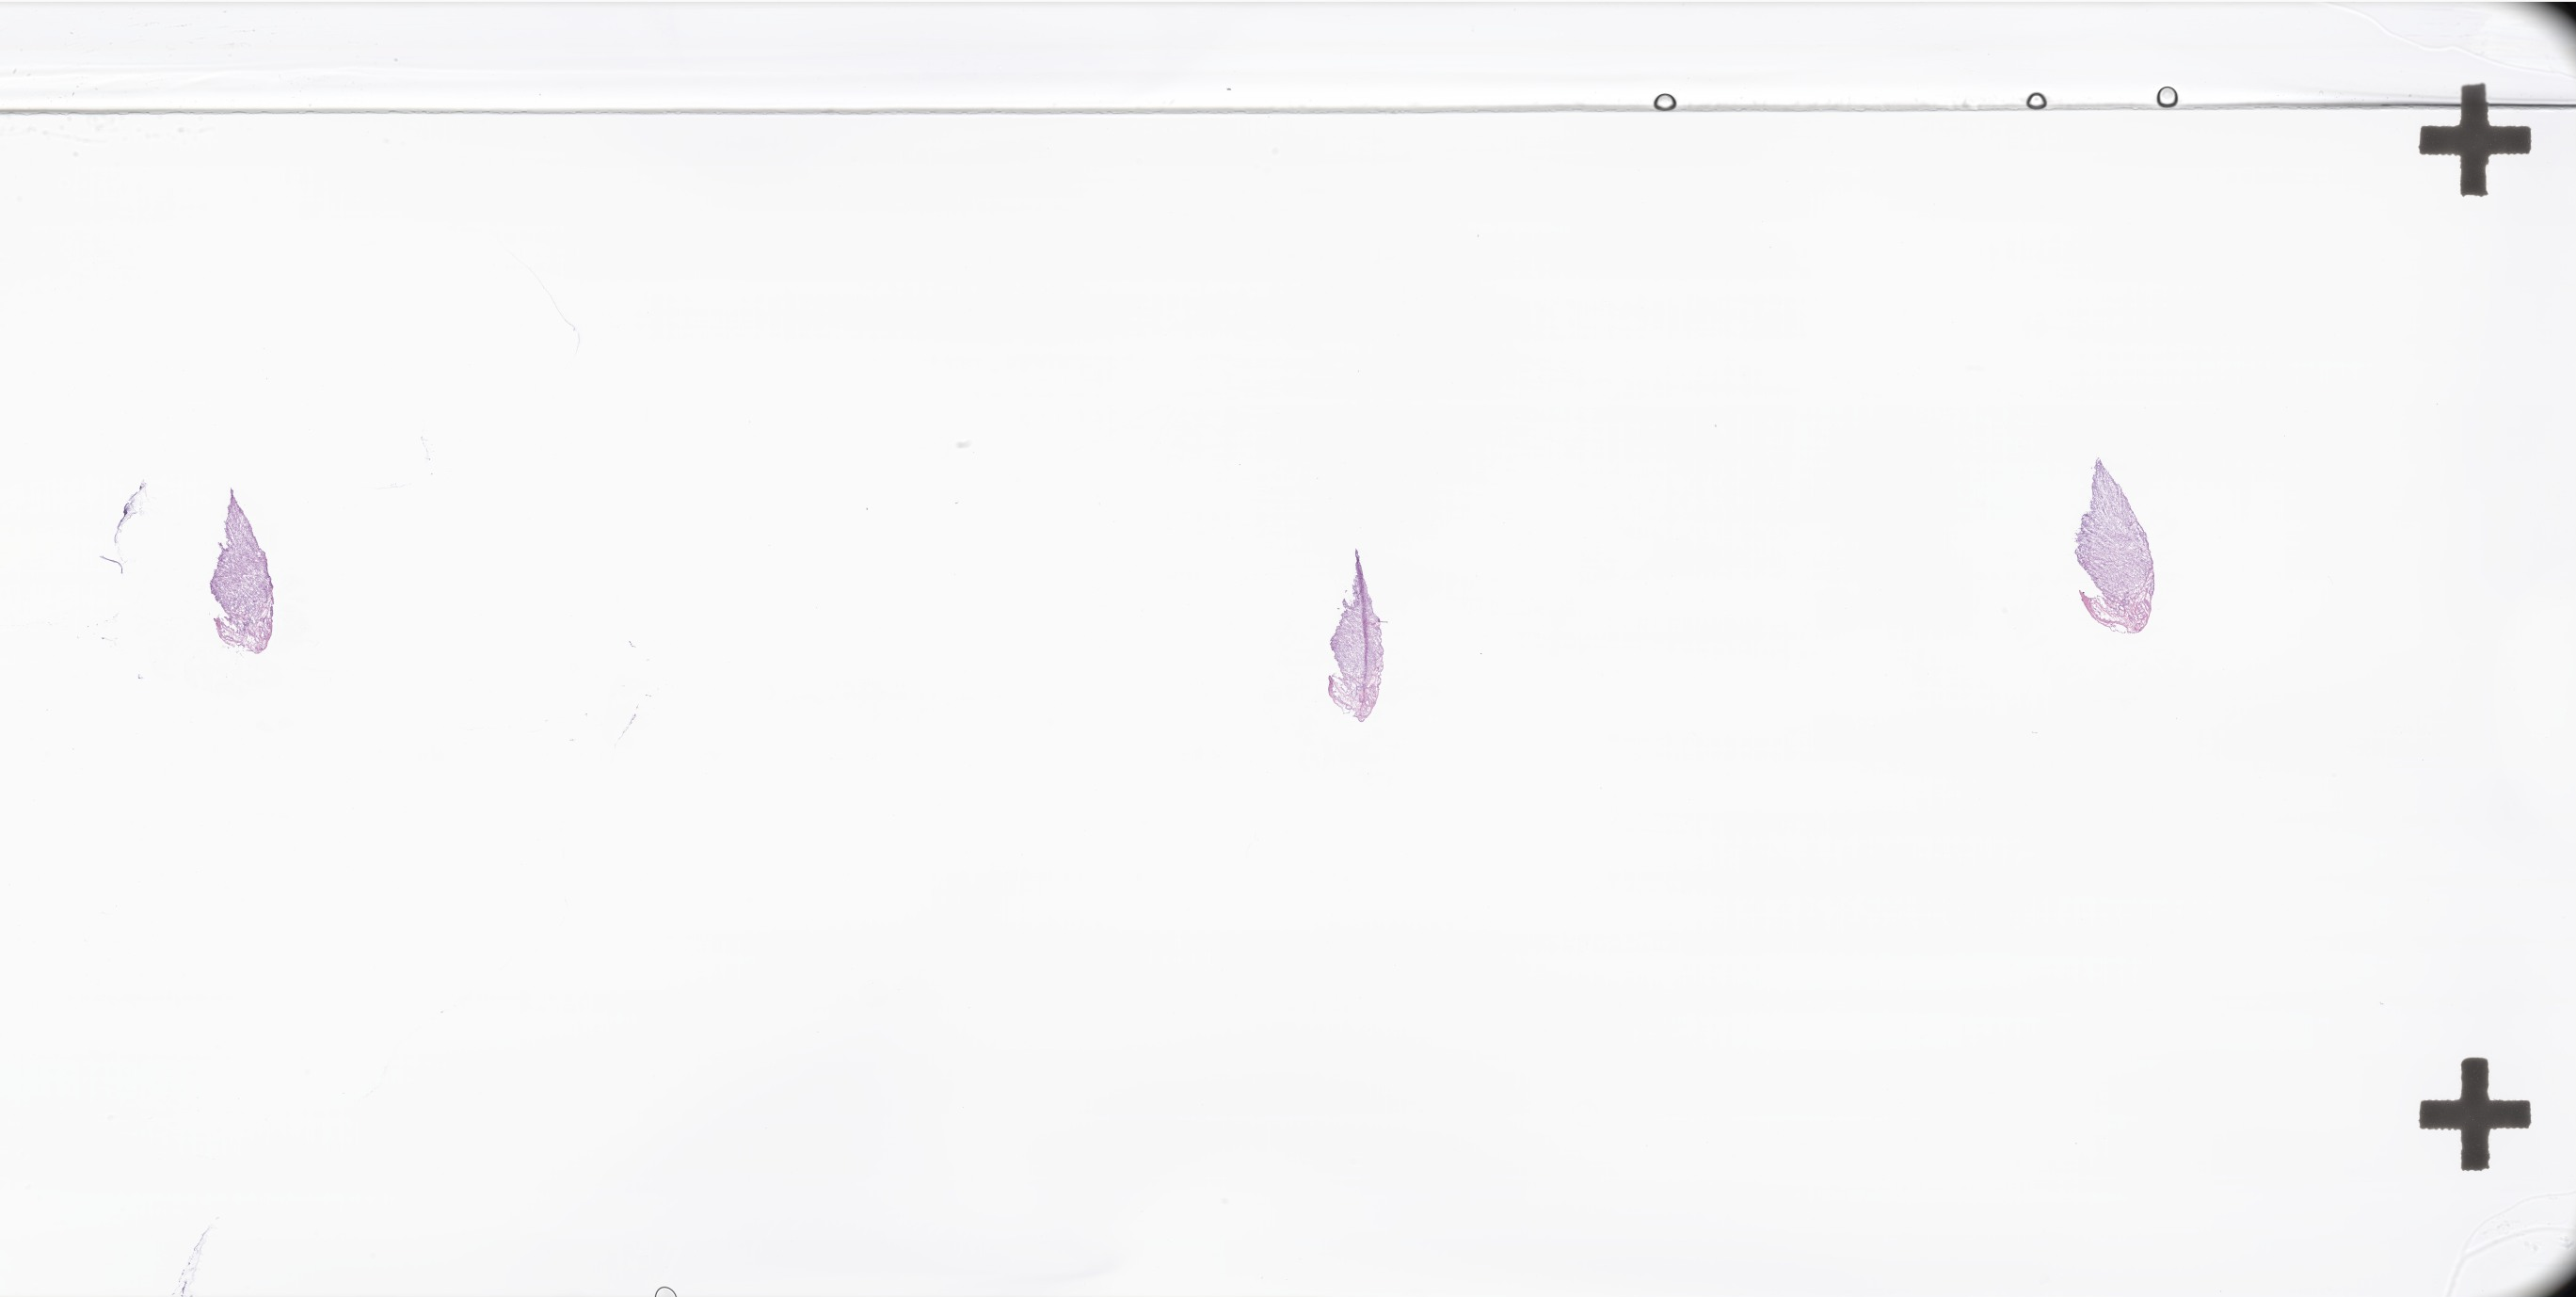
Digitized H&E-stained section of tumor tissue from the pelvis, a low-resolution overview of the entire scanned area, about 46.2 x 23.2 mm; frozen section (OCT-embedded). Male patient, age 207 months (17 years 3 months).
Diagnosis: Epithelioid sarcoma, NOS.